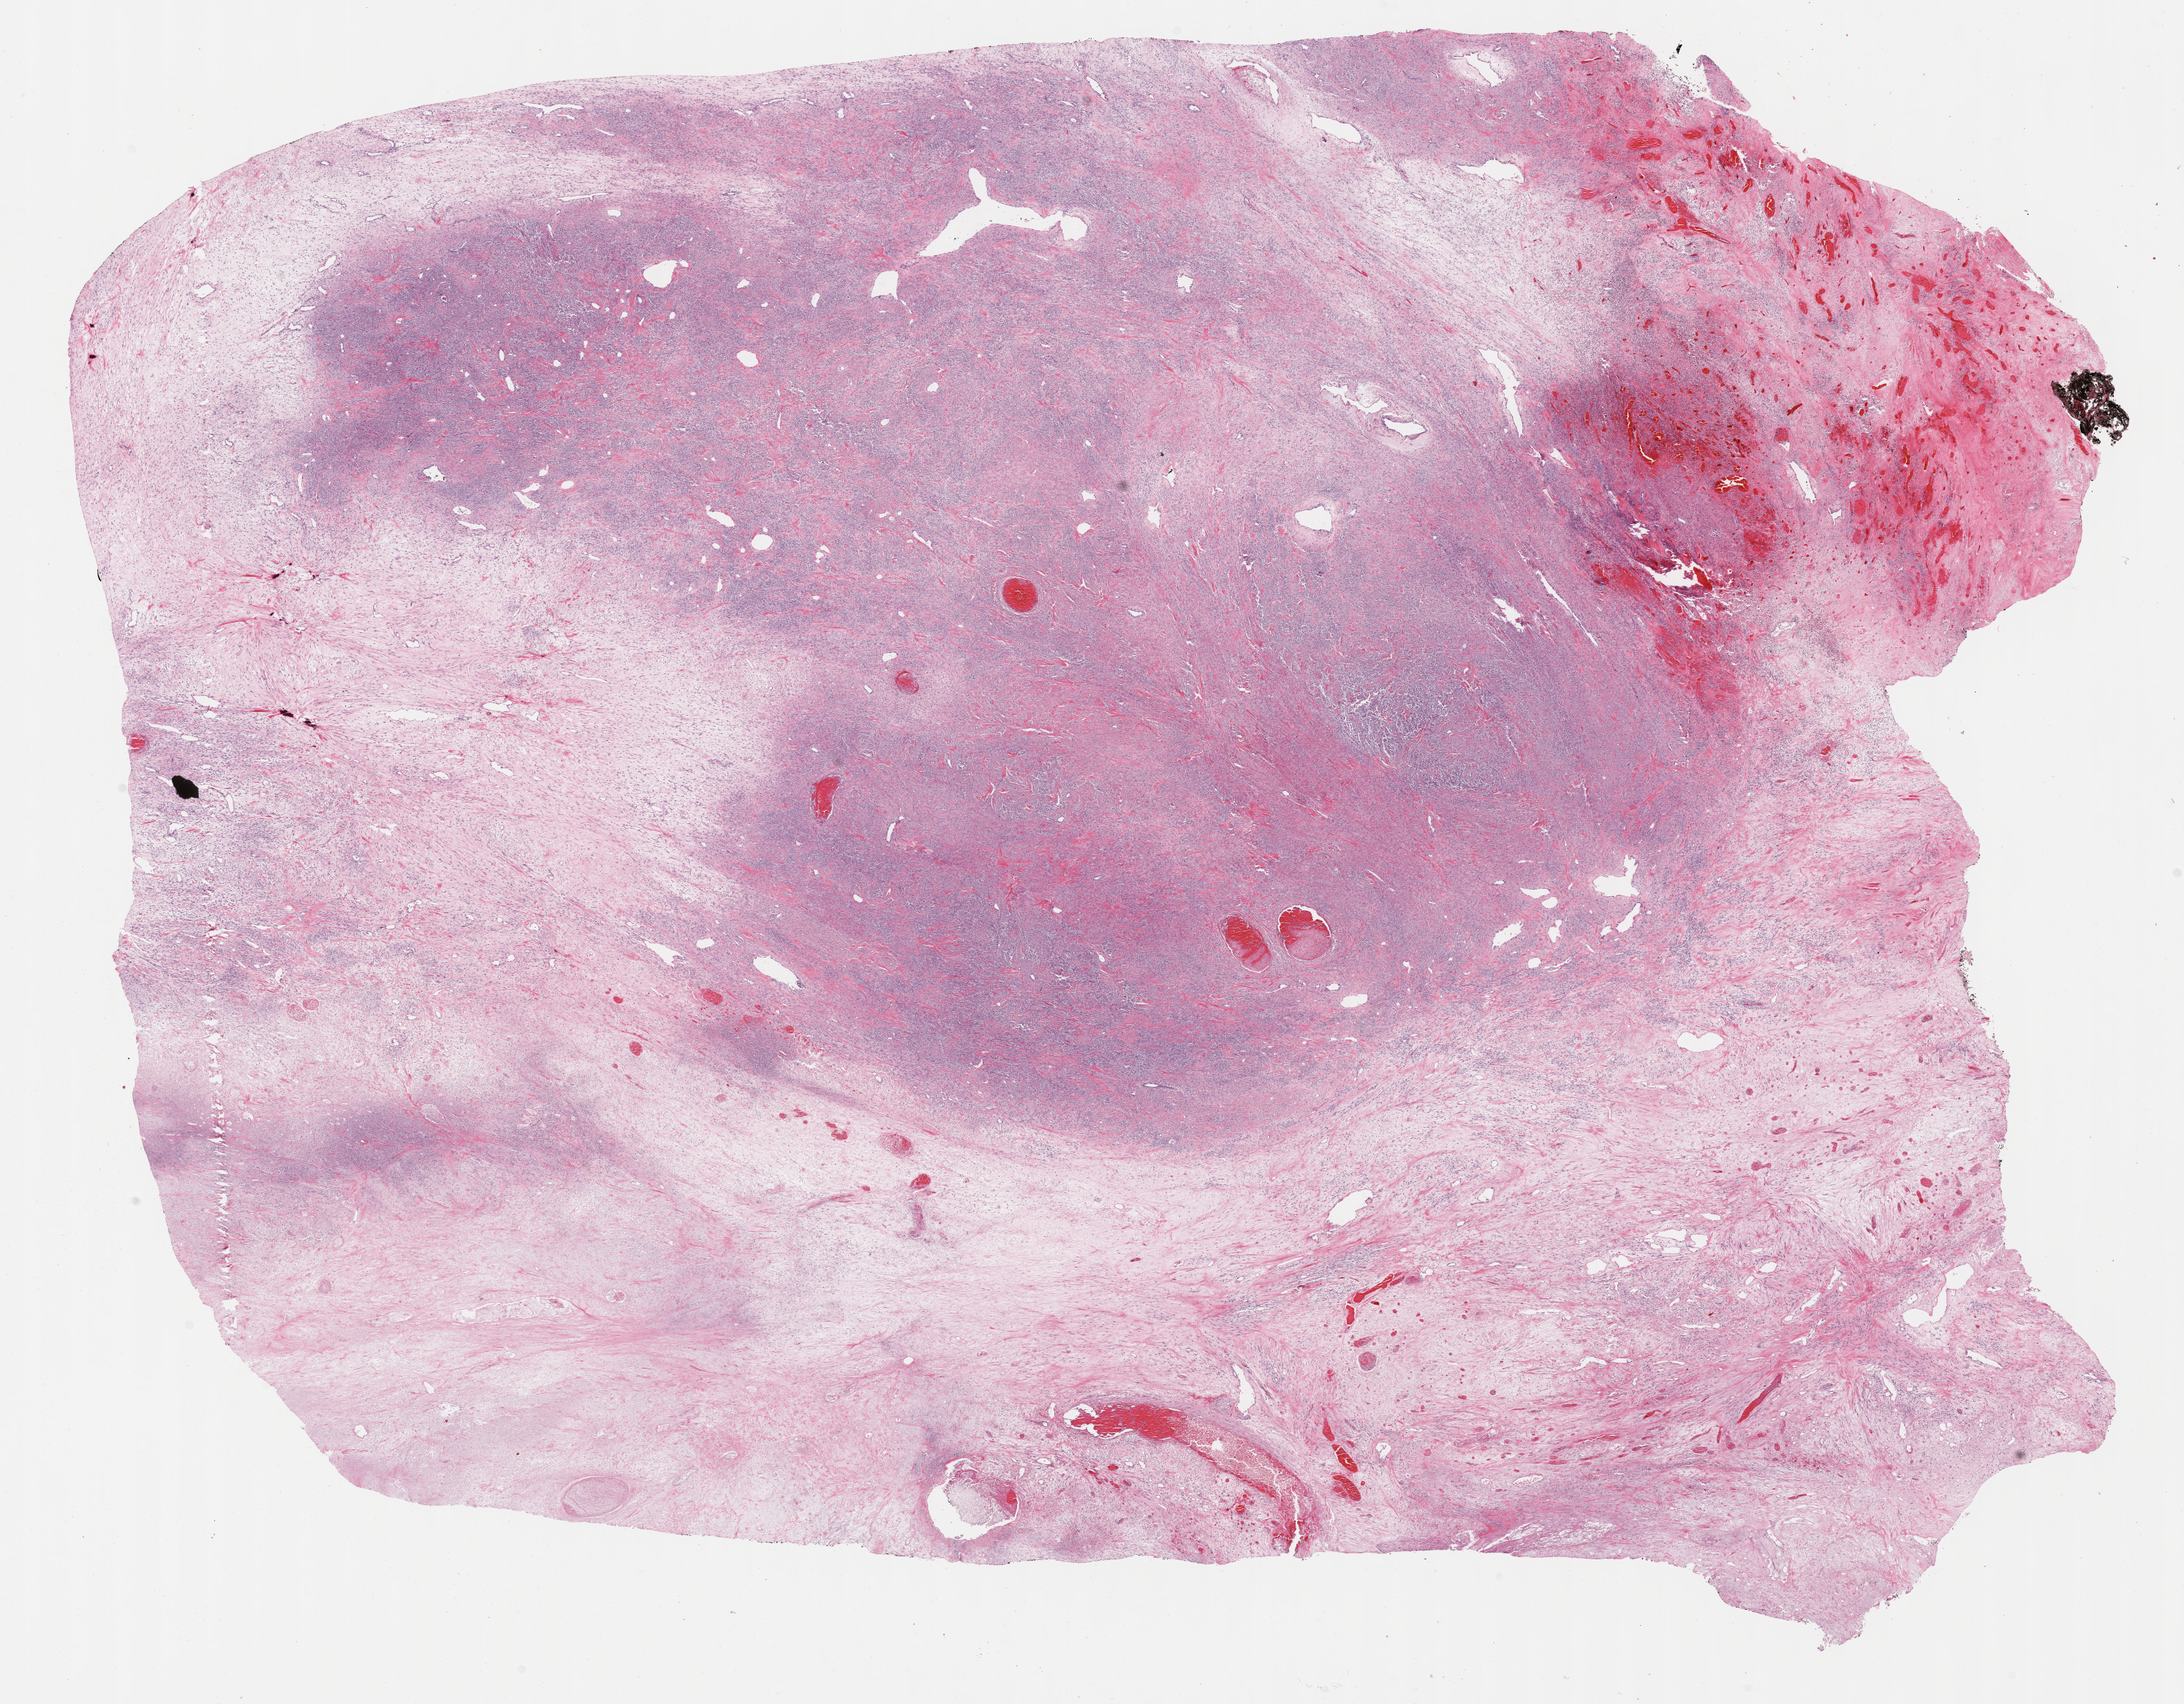
Whole-slide histology image, H&E — shown as a low-resolution overview of the whole scanned area (about 24.2 x 18.9 mm, slide scanned at 40x), formalin-fixed paraffin-embedded (FFPE) diagnostic section, retroperitoneum and peritoneum, primary tumour sample. Patient: female, age at initial diagnosis 71 years.
- pathologic diagnosis: Undifferentiated sarcoma (retroperitoneum)